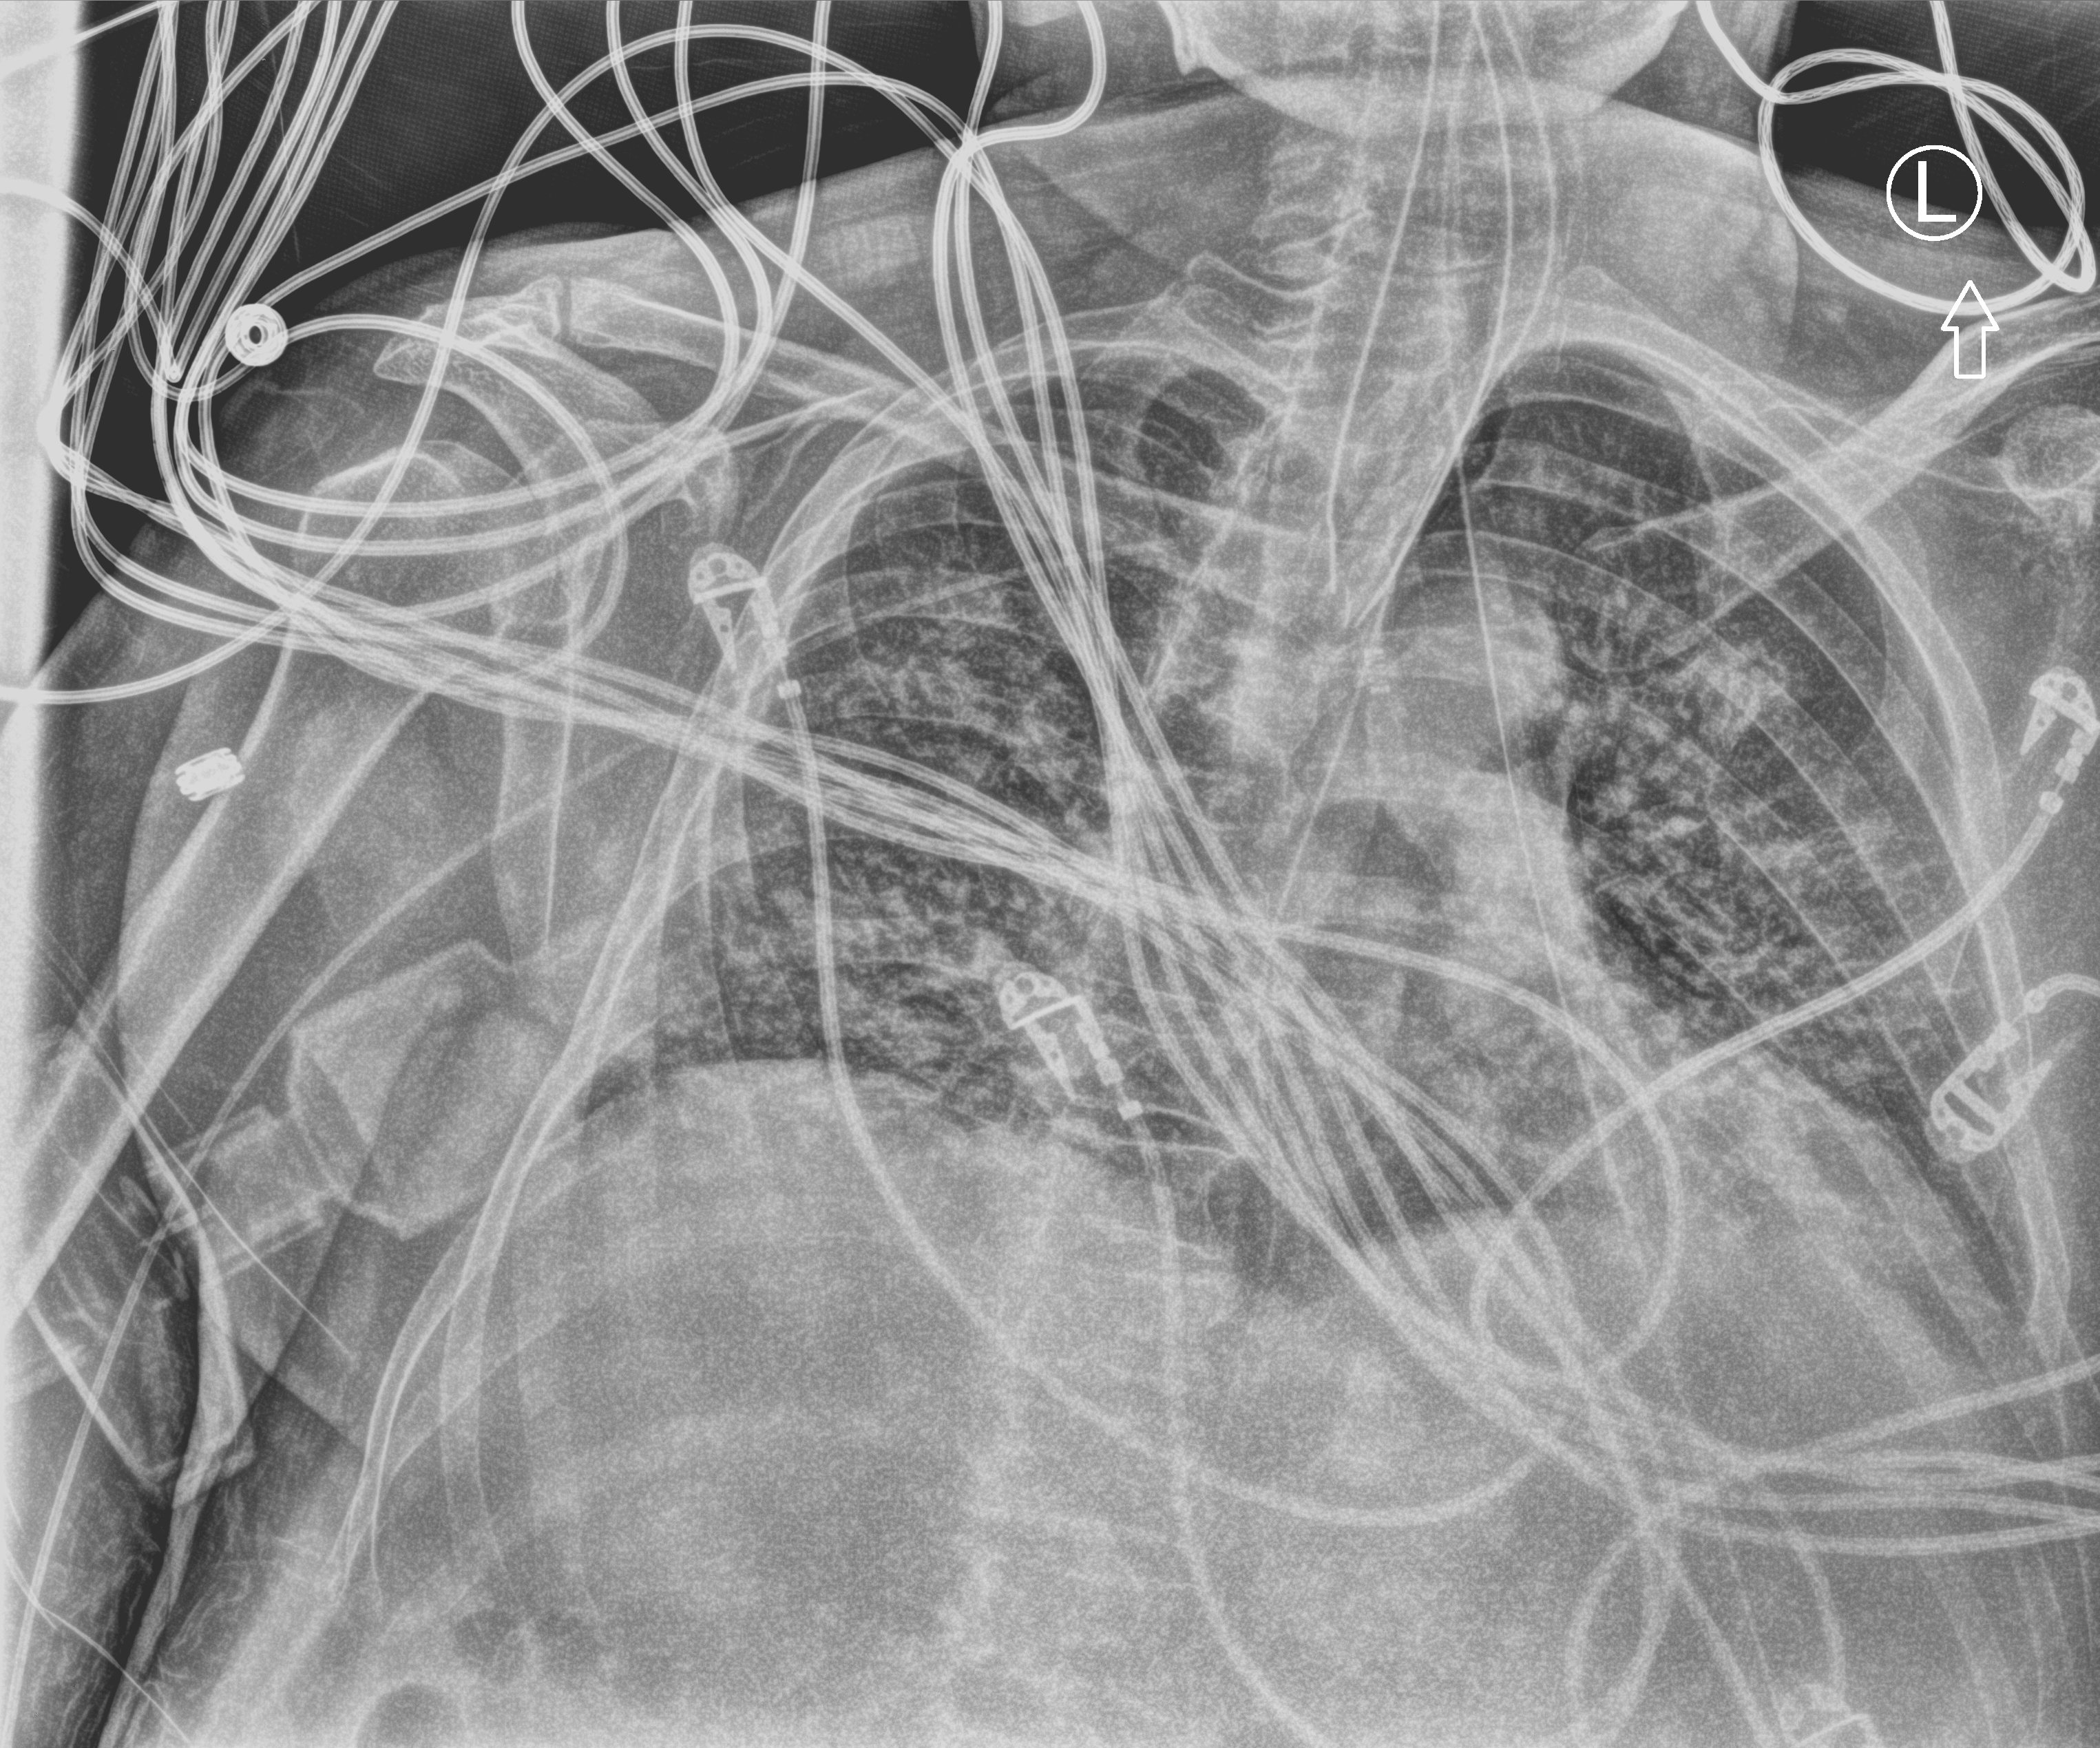
Chest X-ray (portable), anteroposterior (AP) projection. Patient hospitalised with COVID-19; male, aged 60–74 years.
Hospital-stay facts (about this admission, not read from this image; timing relative to this image not recorded):
- mechanically ventilated during this hospital stay: yes